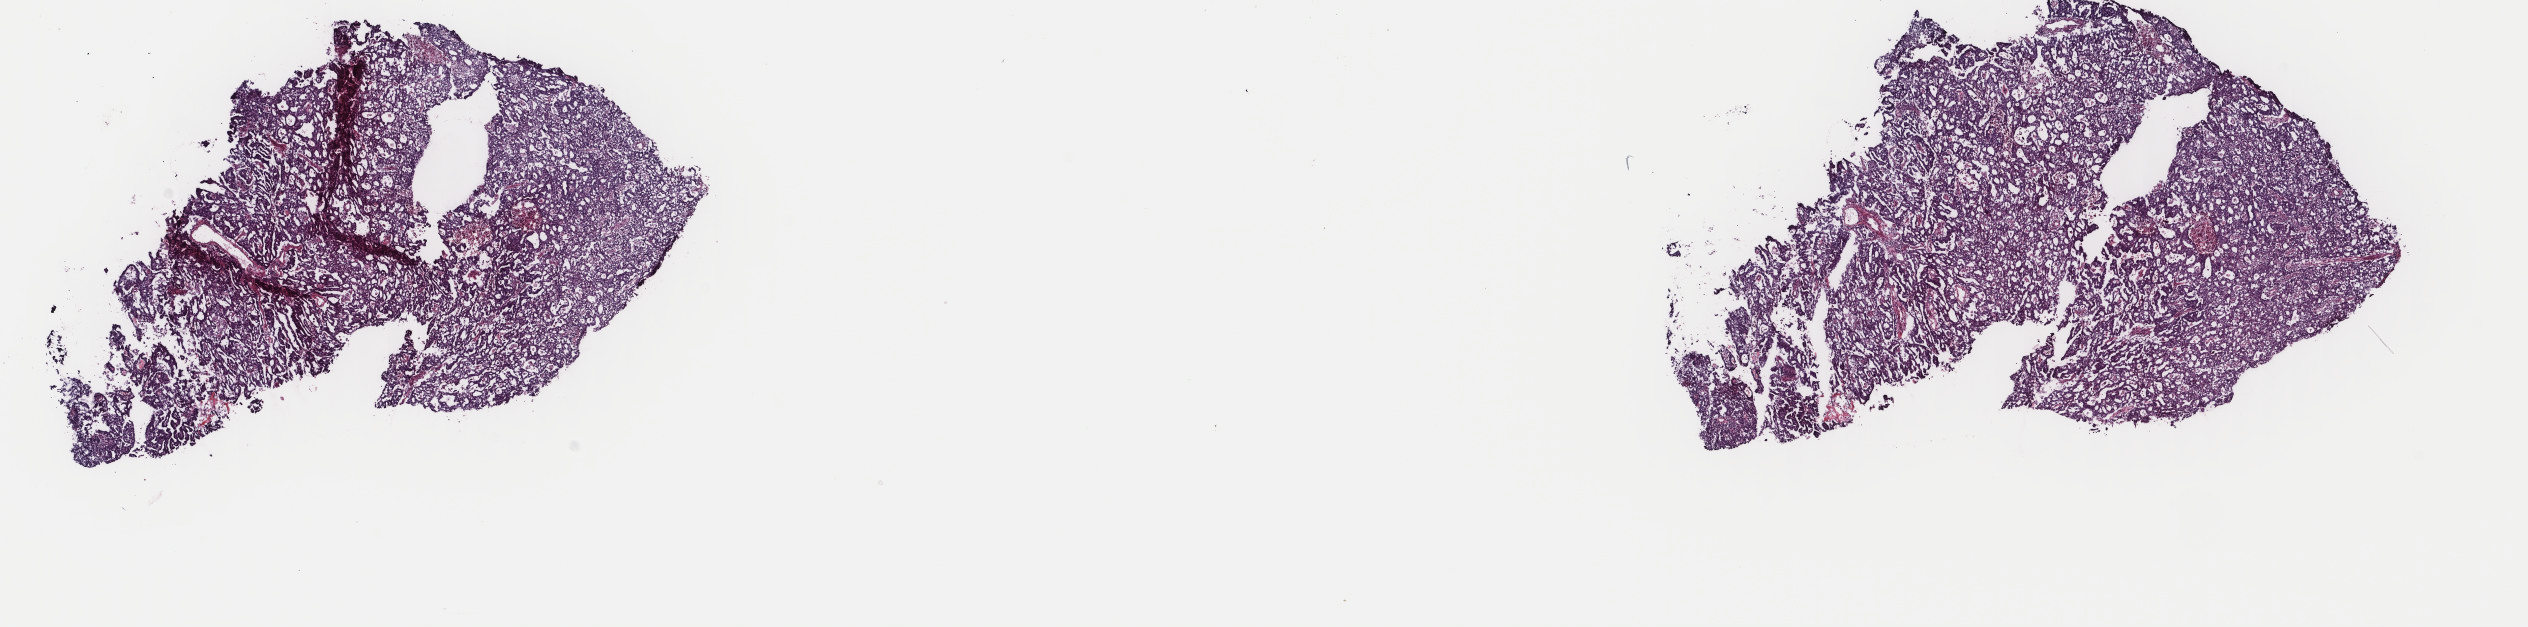
Whole-slide histology image, H&E-stained, a low-resolution overview of the entire scanned area, about 20.1 x 5.0 mm (acquisition: 40x scan), frozen section from the top of the tissue portion, uterus, primary tumour sample. Female, age 73 years at initial diagnosis. Histologic grade: G3 (poorly differentiated). Pathologist review of this section (percent, as recorded): tumour cells 90%, tumour nuclei 90%, normal cells 0%, stromal cells 10%, necrosis 0%. Infiltration values recorded for this section: lymphocyte infiltration 0%, monocyte infiltration 5%, neutrophil infiltration 0%.
• lymph nodes positive (case pathology): 0 of 9 examined
• FIGO stage: IB
• pathologic diagnosis: Endometrioid adenocarcinoma, NOS (endometrium)